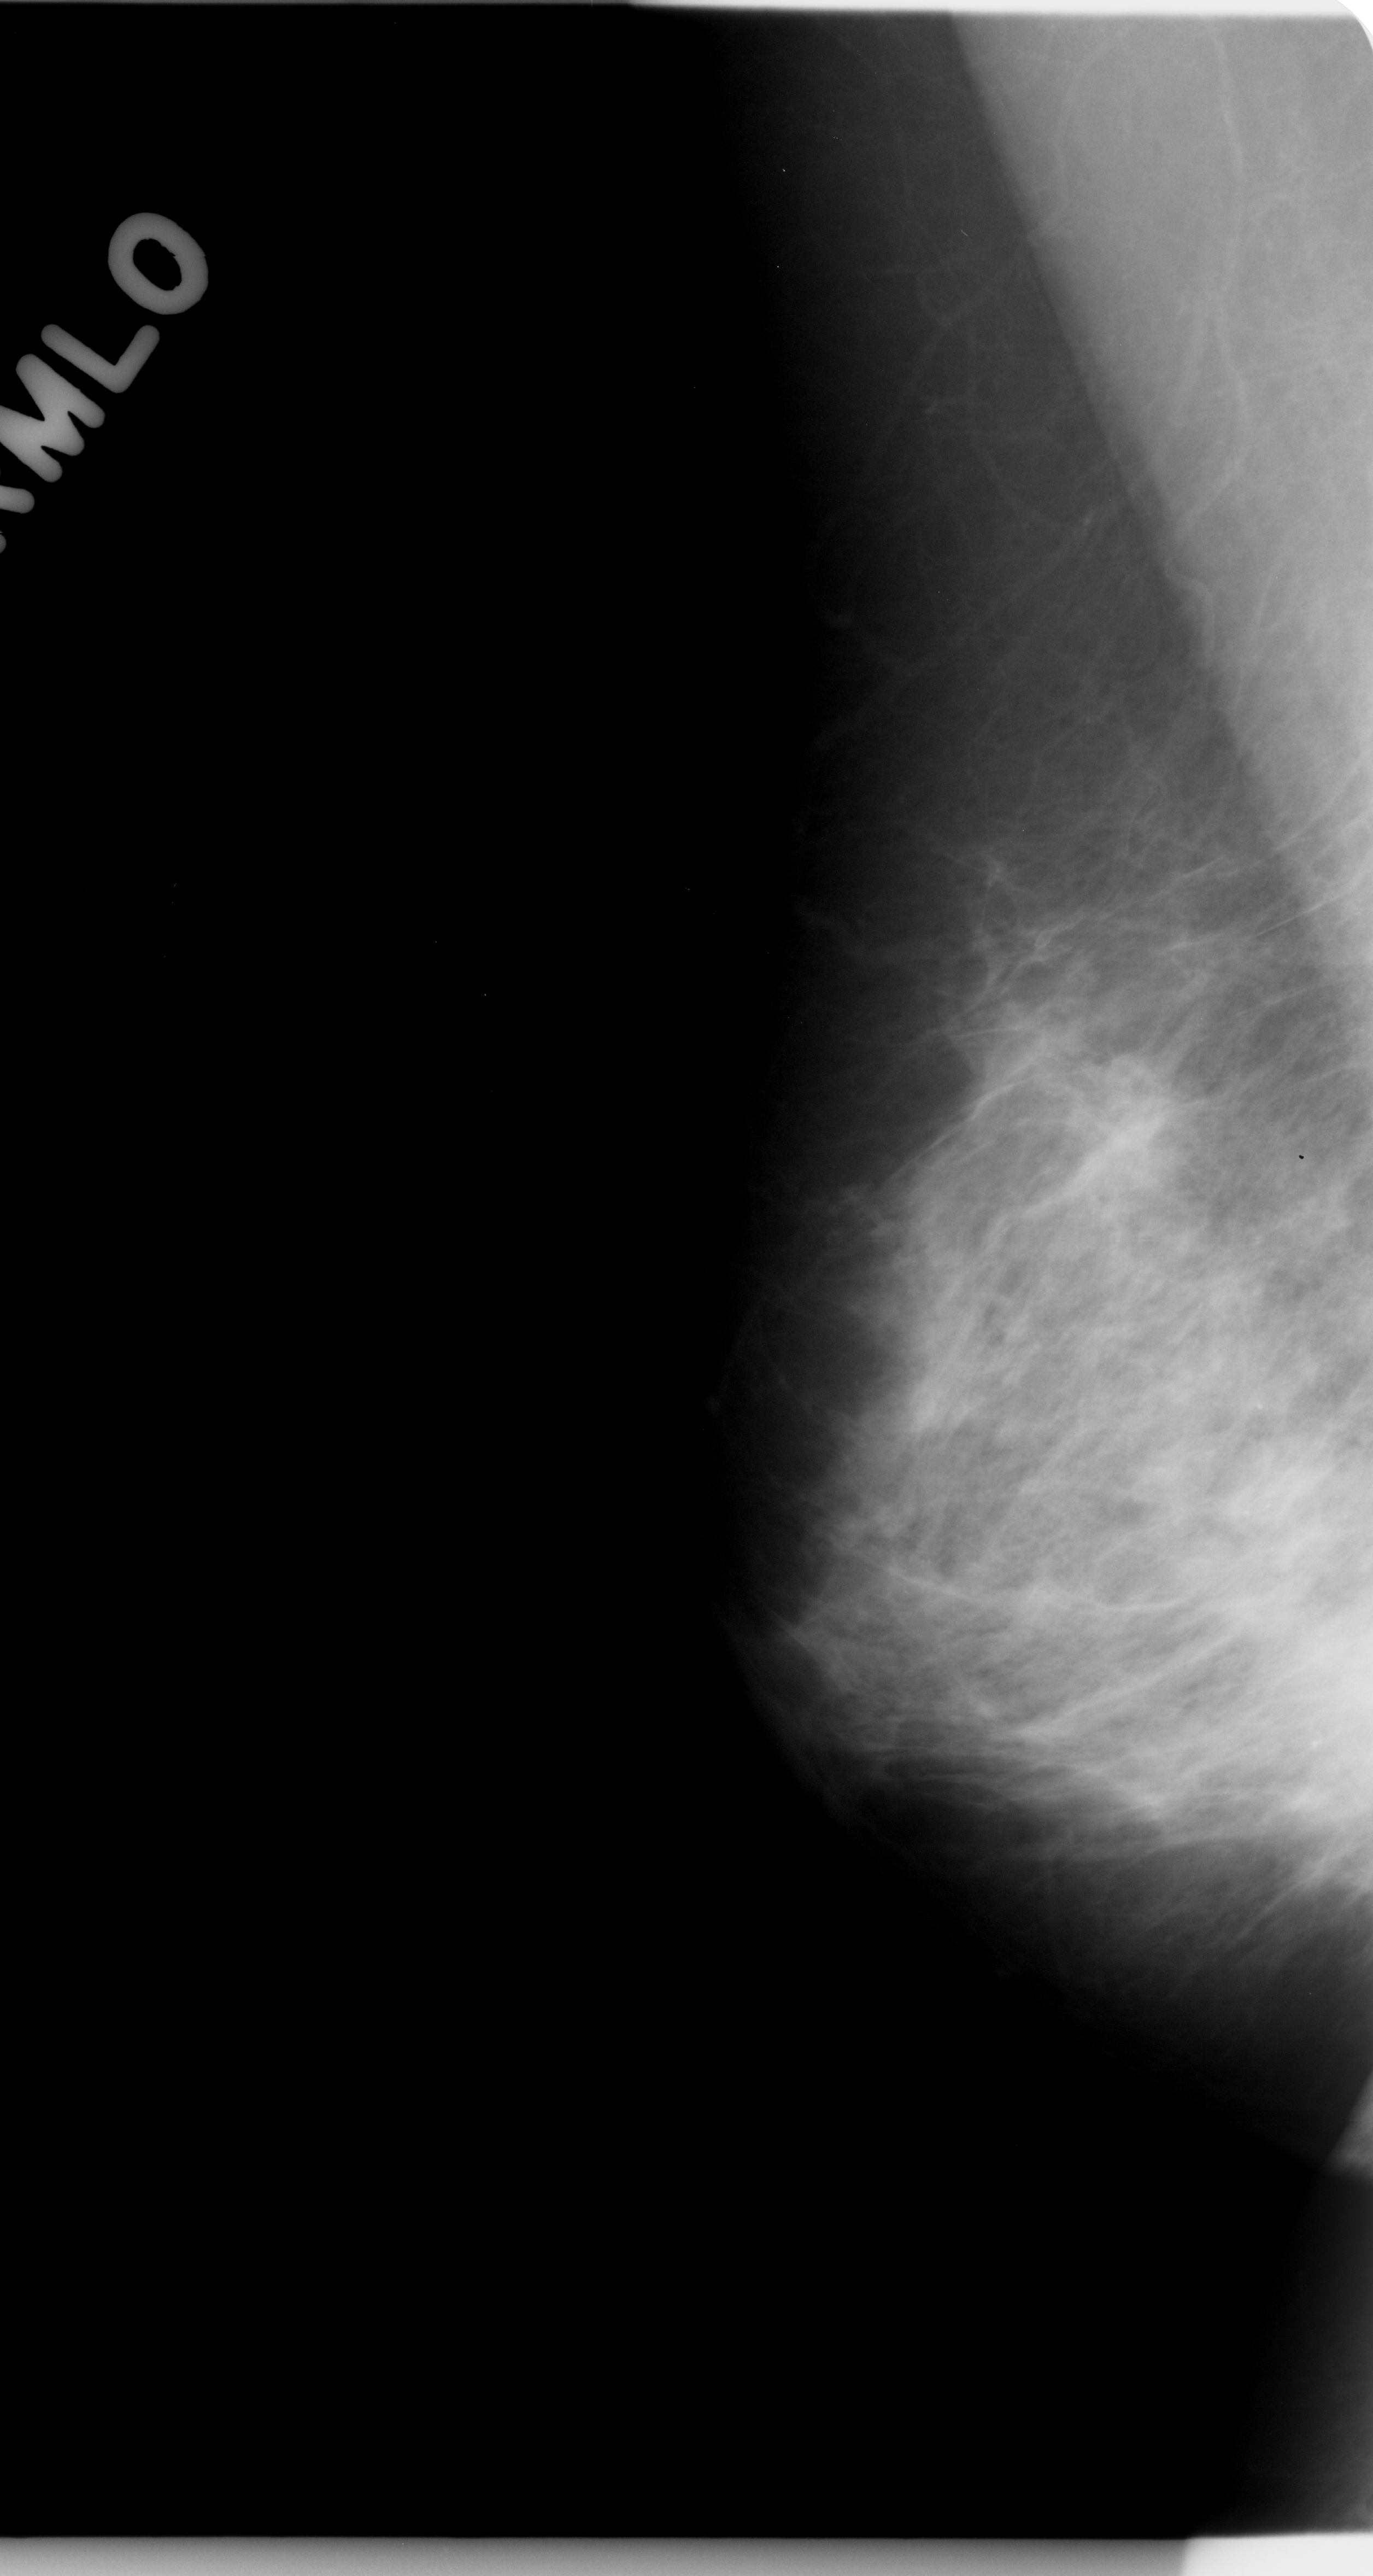
Mammogram (digitized film); right breast; MLO view; BI-RADS breast density category 3 (scale 1–4); 1373 × 2576 image matrix.
Expert-marked regions of interest on this film, with their recorded descriptors:
- mass, shape irregular, margins ill defined; BI-RADS assessment category 4; pathology (as recorded): malignant: bounding box <1028,1042,1212,1226> (left, top, right, bottom; pixels)